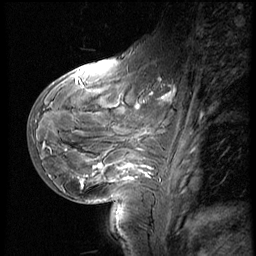
Breast MRI (dynamic contrast-enhanced), one sagittal slice; position 22 of 60 along the scan axis; 3 images stored at this slice position (order not interpretable as contrast timing); 1.5 T; TE 4.2 ms, TR 8.9 ms; 2.5 mm slice thickness; 256 × 256 image matrix, field of view 200 × 200 mm. Patient: female, 29 years. From the clinical record (not read from this slice): setting: breast cancer imaged before/during neoadjuvant chemotherapy.
Outlined on this slice (semi-automatic segmentation, software-assisted and operator-edited):
- analysis volume of interest (the breast-tissue region the enhancement analysis was run in; not a lesion): bounding box <29,57,185,200> (left, top, right, bottom; pixels)
- tumour enhancement mask (voxels above the 140 % enhancement threshold inside the analysis volume of interest): <82,95,169,186>